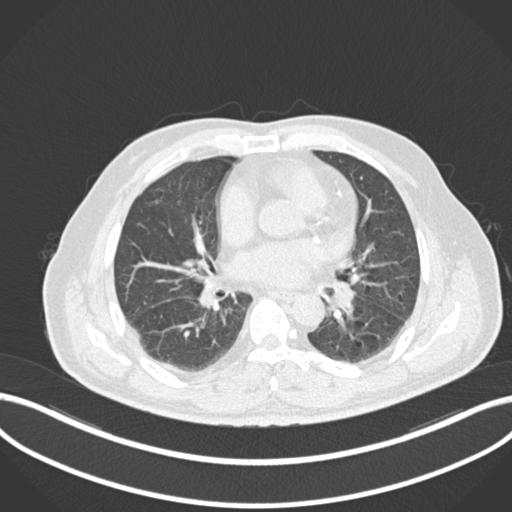
Chest CT, one axial slice. Slice 66 of 161 in the series (ordered by position). Reconstruction kernel B30f. Lung window (W 1500 / L -600 HU). 1 mm slice thickness. 512 × 512 image matrix, field of view 400 × 400 mm. Patient: male, 71 years. Case-level facts recorded for this patient, not image findings: clinical TNM (as recorded): T1b N0 M0.
Outlined on this slice (bounding box drawn by a radiologist):
- lung tumour (recorded histology: squamous cell carcinoma): box from (x=330, y=278) to (x=358, y=319) px